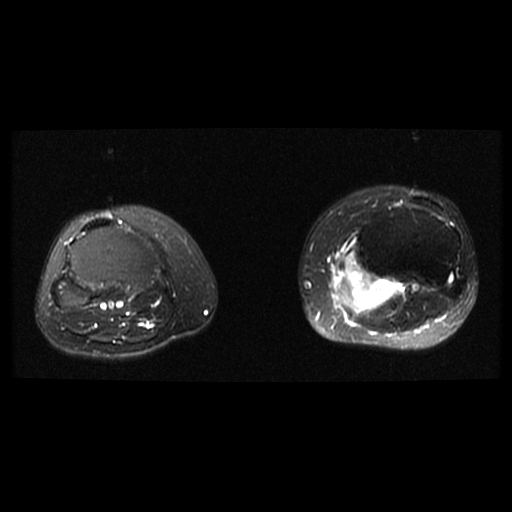
MRI of an extremity soft-tissue mass, one axial slice; slice 24 of 38 in the series (ordered by position); T2-weighted fat-saturated; 512 × 512 image matrix. Female patient. Case-level facts recorded for this patient, not image findings: histological type: extraskeletal high grade osteogenic sarcoma; grade: high; site of the primary tumour: left calf.
Structures marked on this image (manually delineated by an expert):
- gross tumour volume (mass): bounding box <334,264,397,313> (left, top, right, bottom; pixels)